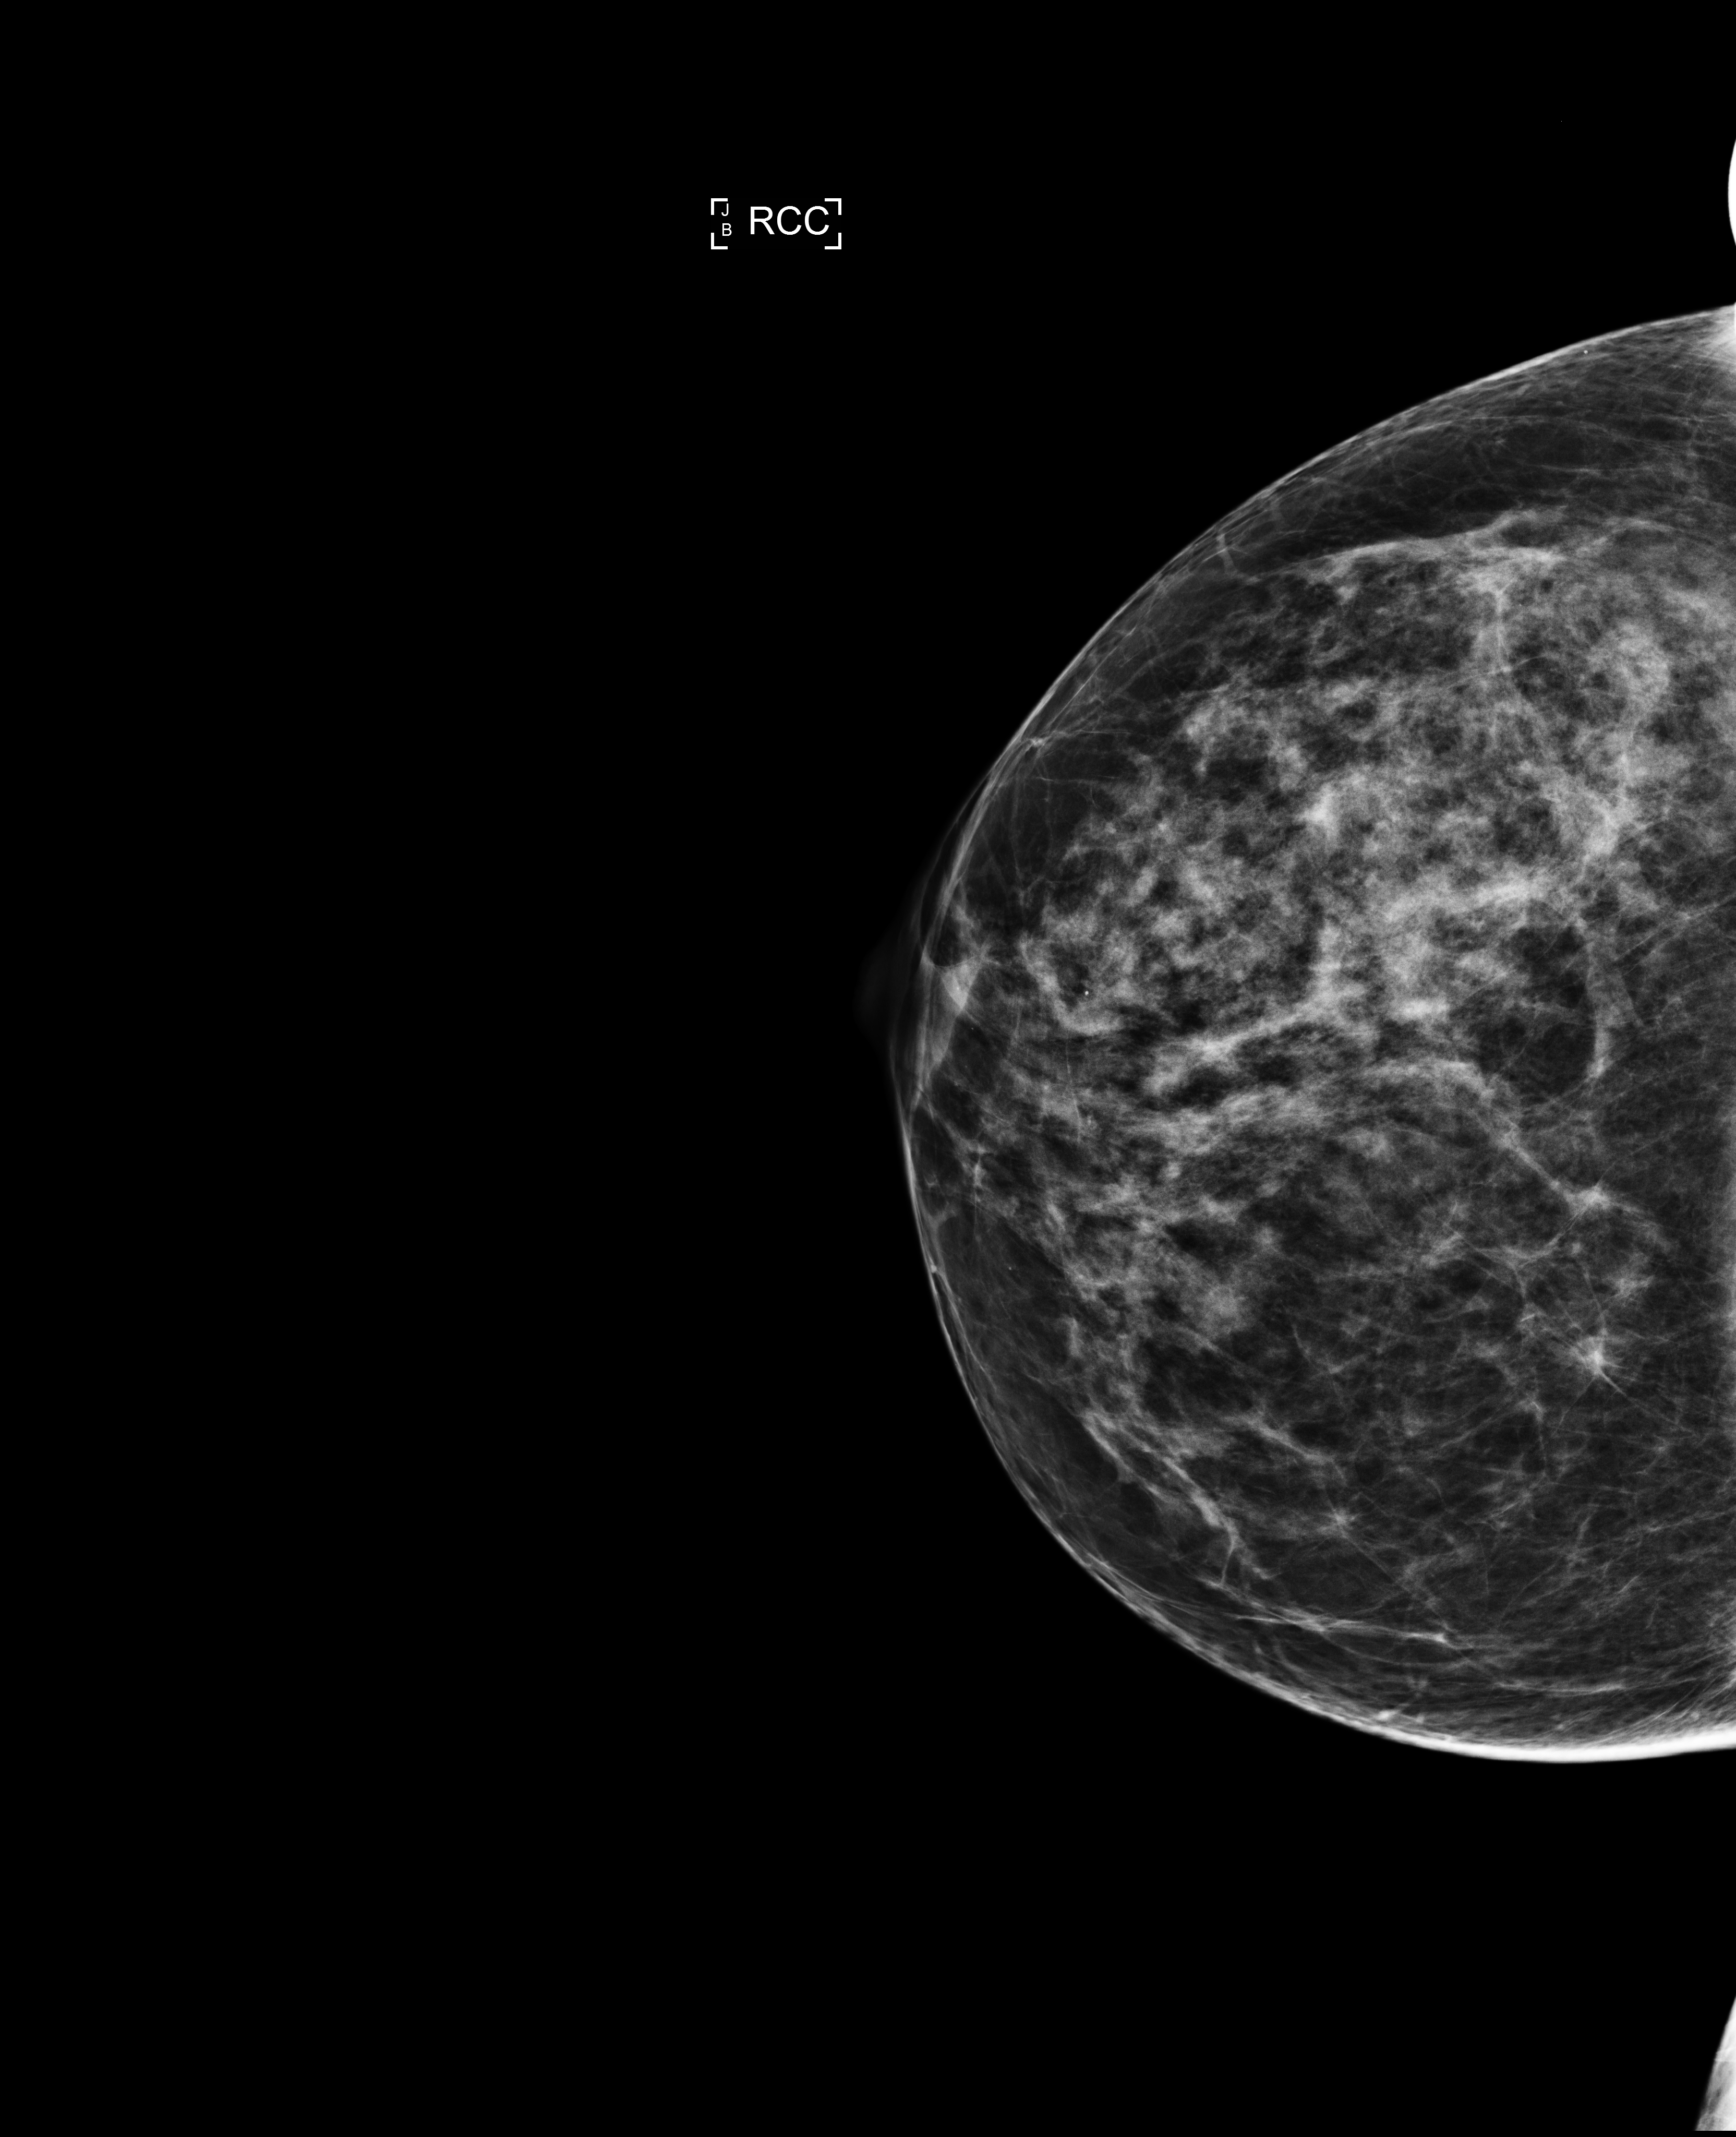
Full-field digital mammogram (FFDM), right breast, craniocaudal (CC) view, screening examination. Female patient, age 47 years.
BI-RADS breast density category at the screening exam (both breasts, scale 1–4): 3. Final BI-RADS assessment for this screening round (tomosynthesis exam, both breasts): category 1. Recall: no recall after this screen.